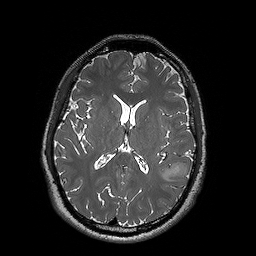
Brain MRI from a brain-tumour surgery series, one axial slice; position 79 of 192 along the scan axis; 1 mm slice thickness; 256 × 256 image matrix, field of view 250 × 250 mm. From the clinical record (not read from this slice): histopathology: Oligodendroglioma; WHO grade: 2; IDH mutation: yes; tumour location: Left Posterior Temporal.
Outlined on this slice (manually delineated by an expert):
- tumour: bounding box [x1, y1, x2, y2] px = [159, 162, 193, 181]